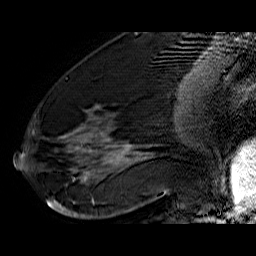
Breast MRI (dynamic contrast-enhanced), one sagittal slice; position 25 of 60 along the scan axis; dynamic contrast-enhanced series, time point 2 of 6 at this slice position (early post-contrast); 1.5 T; TE 6.4 ms, TR 32.9 ms; 256 × 256 image matrix, field of view 200 × 200 mm. Female patient. Case-level facts recorded for this patient, not image findings: setting: breast cancer imaged before/during neoadjuvant chemotherapy; receptor status: HR-positive, HER2-negative.
Outlined on this slice (semi-automatic segmentation, software-assisted and operator-edited):
- analysis volume of interest (the breast-tissue region the enhancement analysis was run in; not a lesion): bounding box (x1, y1, x2, y2) in pixels: (41, 74, 176, 210)
- tumour enhancement mask (voxels above the 100 % enhancement threshold inside the analysis volume of interest): (46, 106, 136, 210)